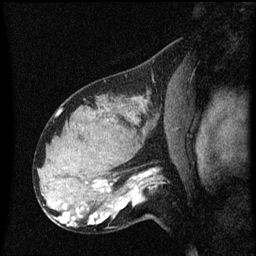
Breast MRI (dynamic contrast-enhanced), one sagittal slice; position 37 of 60 along the scan axis; dynamic contrast-enhanced series, image 2 of 3 at this slice position (ordered by acquisition); 1.5 T; TE 4.2 ms, TR 8.4 ms; 2 mm slice thickness; 256 × 256 image matrix, field of view 200 × 200 mm. Patient: female, 31 years. Case-level facts recorded for this patient, not image findings: setting: breast cancer imaged before/during neoadjuvant chemotherapy; receptor status: HR-positive, HER2-negative.
Structures marked on this image (semi-automatically segmented with operator editing):
- analysis volume of interest (the breast-tissue region the enhancement analysis was run in; not a lesion): box from (x=102, y=166) to (x=169, y=223) px
- tumour enhancement mask (voxels above the 70 % enhancement threshold inside the analysis volume of interest): (x=102, y=170)–(x=156, y=221)